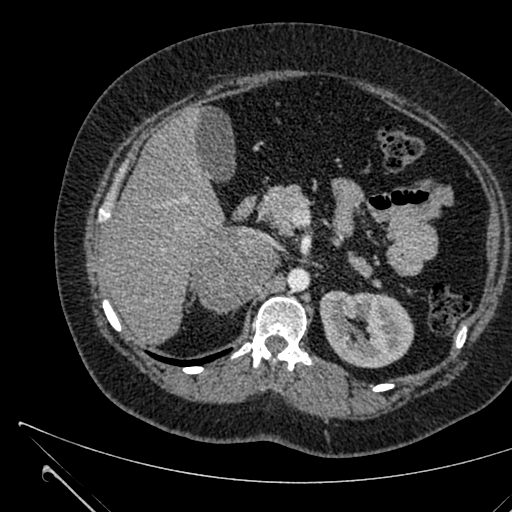
Contrast-enhanced abdominal CT, one axial slice. Slice 404 of 731 in the series (ordered by position). 120 kVp. Intravenous contrast given. Soft-tissue window (W 400 / L 40 HU). 1 mm slice thickness. 512 × 512 image matrix, field of view 376 × 376 mm. Female patient, age 36 years. From the clinical record (not read from this slice): diagnosis: adrenocortical carcinoma; tumour side: right adrenal; tumour size at pathology: 10 cm; Ki-67 index: 20 %; stage (as recorded): 4.
Annotated regions visible in this slice (semi-automatically segmented with operator editing):
- mass: bounding box (x1, y1, x2, y2) in pixels: (192, 227, 278, 311)